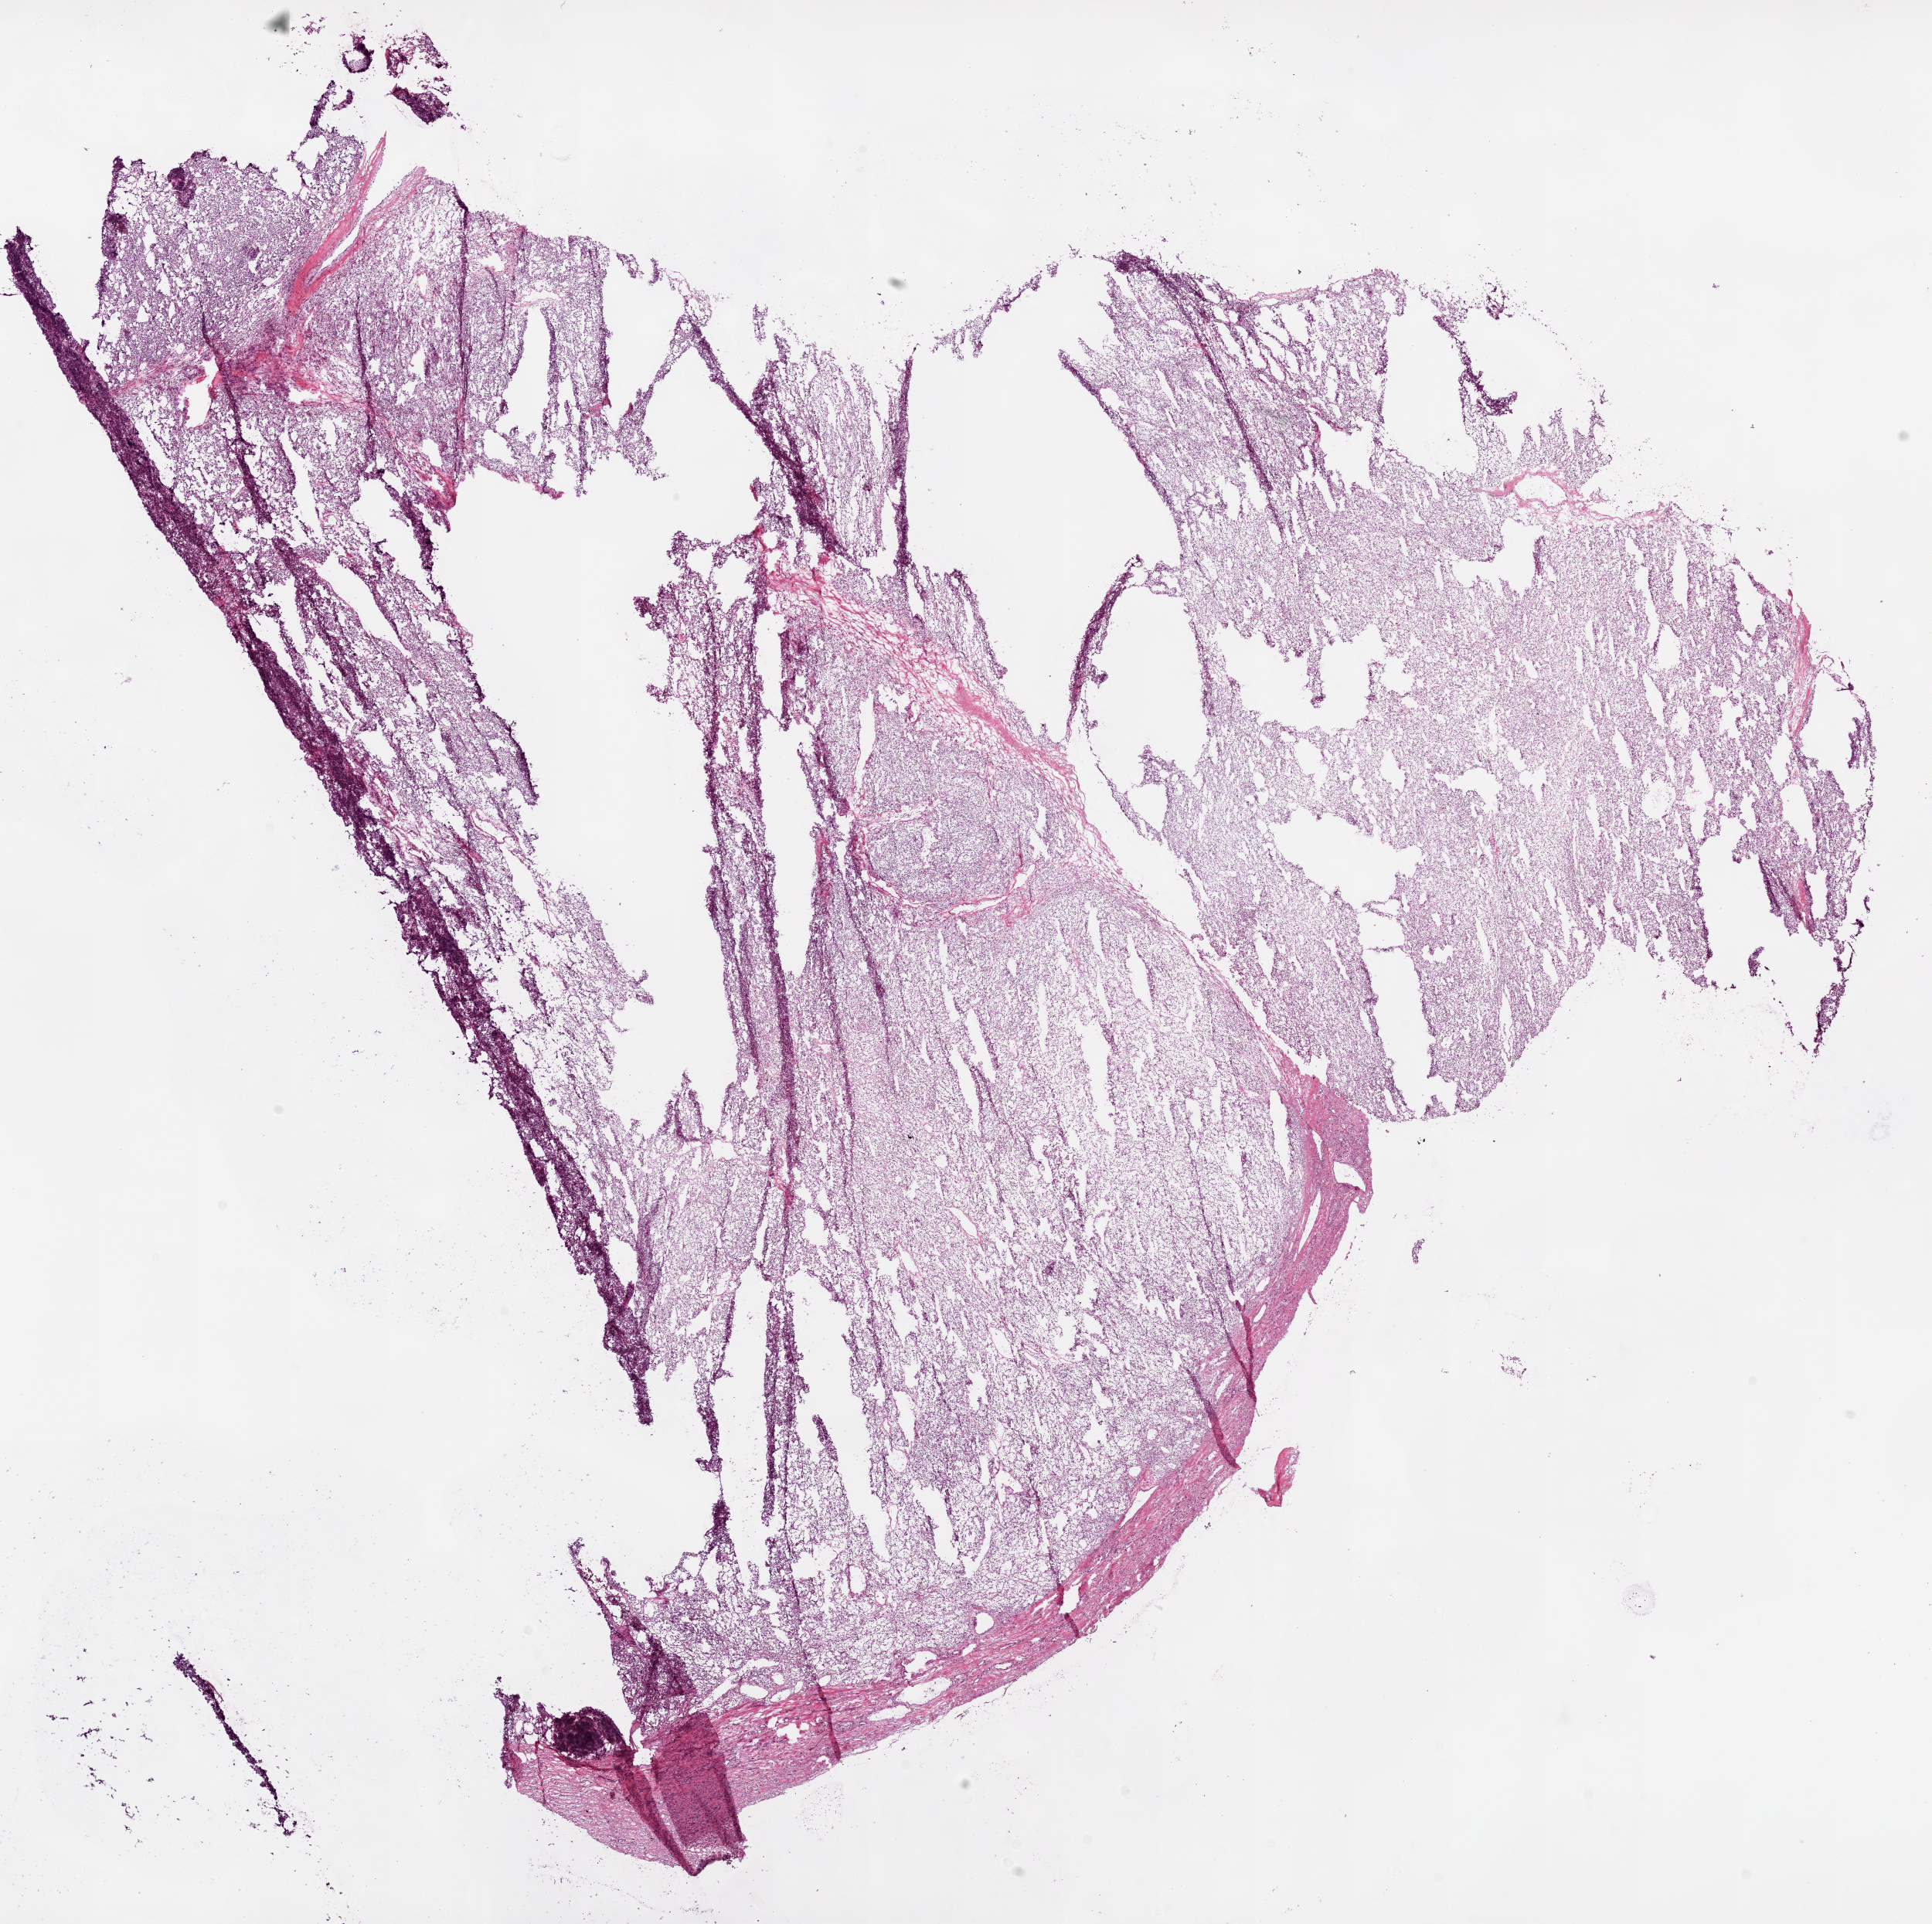
Whole-slide histology image, H&E — shown as a low-resolution overview of the whole scanned area (about 20.1 x 20.0 mm), frozen section, sample: primary tumour, kidney. Patient: female, age at initial diagnosis 61 years. Histologic grade: G2 (moderately differentiated). Slide review estimates, as recorded: tumour cells 88%, tumour nuclei 85%, normal cells 0%, stromal cells 12%, necrosis 0%.
* histologic diagnosis: Clear cell adenocarcinoma, NOS
* AJCC pathologic stage: I (6th edition)